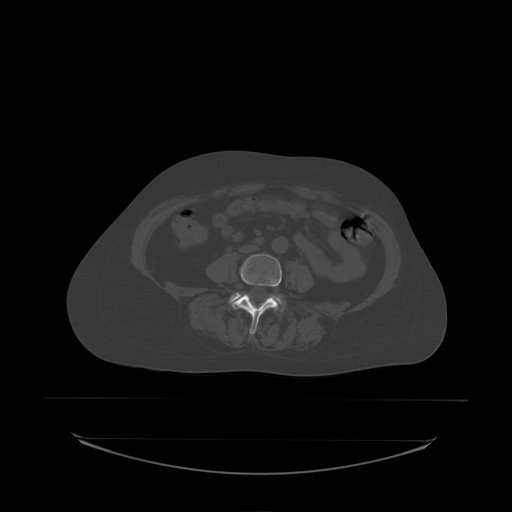
CT including the spine, one axial slice. Position 48 of 242 along the scan axis. Bone window (W 1800 / L 400 HU). 2.5 mm slice thickness. 512 × 512 image matrix, field of view 500 × 500 mm. Patient: female, 53 years. From the clinical record (not read from this slice): primary cancer: lung; vertebrae with lytic lesions (as recorded): T7, L1.
Annotated regions visible in this slice (semi-automatic segmentation, software-assisted and operator-edited):
- L4 vertebra: bounding box <232,254,282,335> (left, top, right, bottom; pixels)
- L5 vertebra: <230,293,284,311>